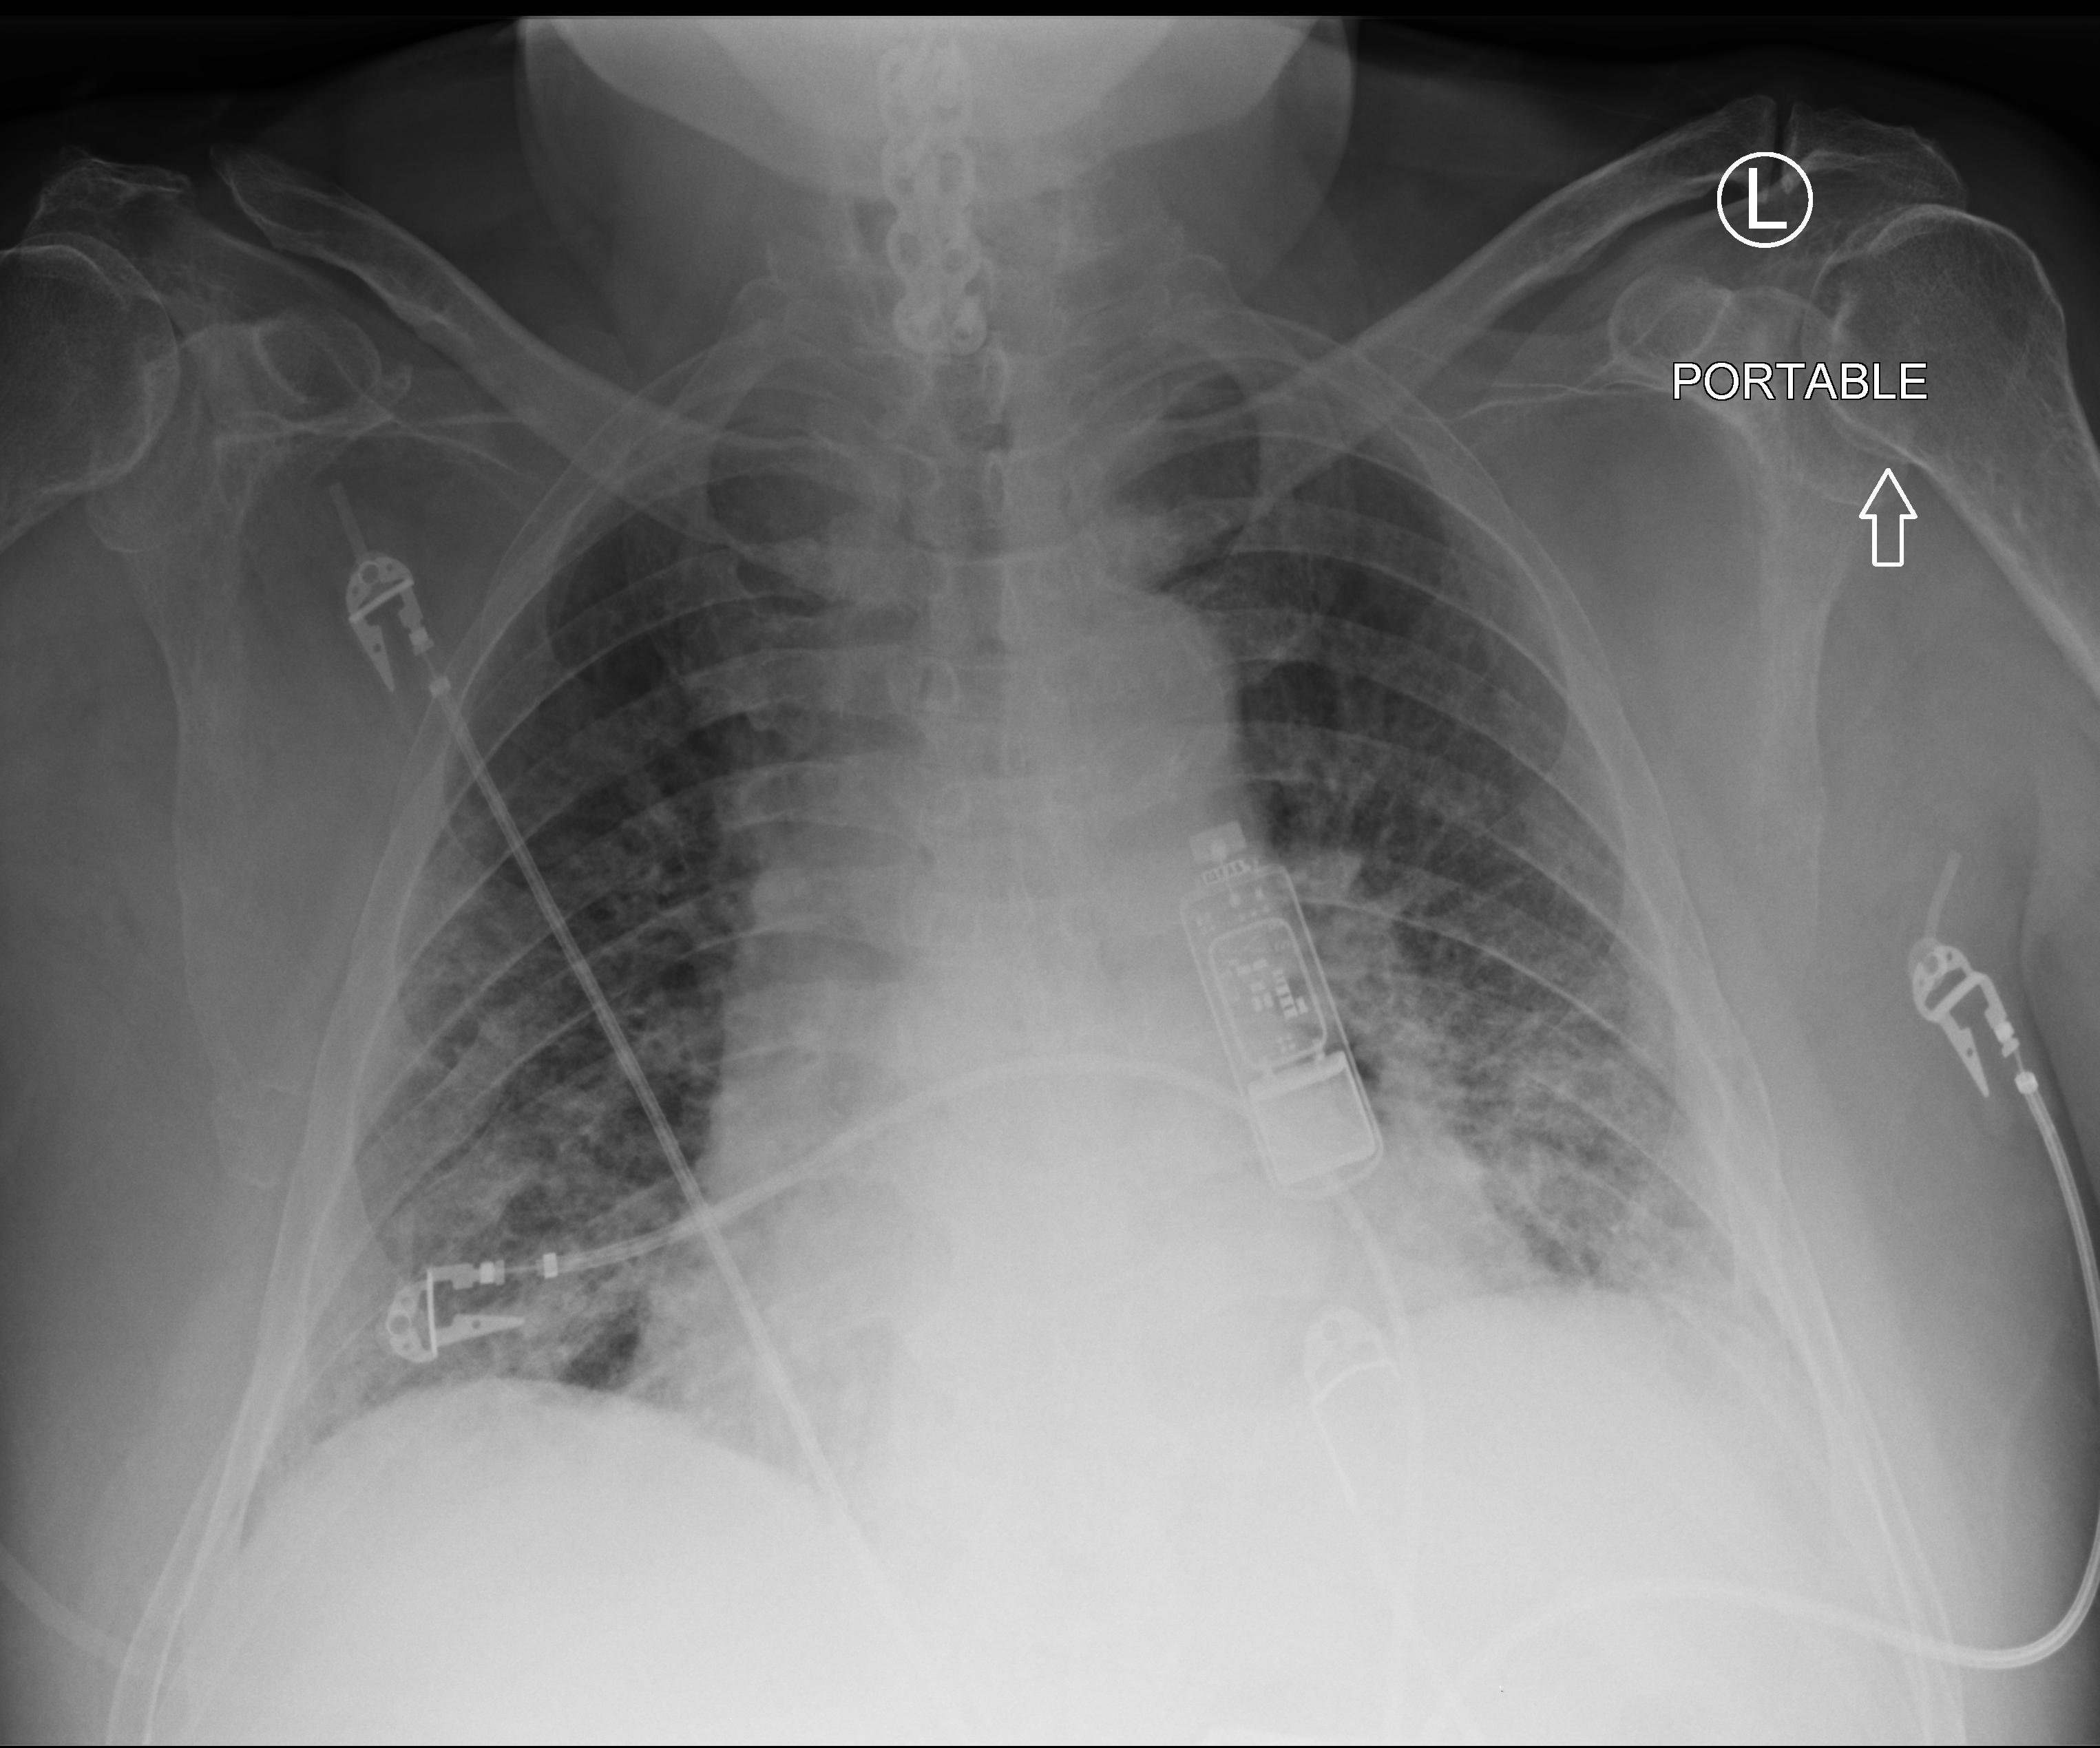
Portable chest radiograph; anteroposterior (AP) projection. Patient hospitalised with COVID-19; male, aged 60–74 years.
From the hospital-stay record, not from the radiograph (when in the stay this image was taken is not recorded): other chronic lung disease (admission record): yes; mechanically ventilated during this hospital stay: yes.